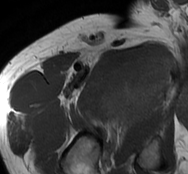
MRI of an extremity soft-tissue mass, one axial slice. Position 68 of 93 along the scan axis. MR volume resampled by the dataset authors to the PET/CT grid (not the native acquisition matrix). 3.27 mm slice thickness. 188 × 174 image matrix, field of view 184 × 170 mm. Male patient. From the clinical record (not read from this slice): histological type: undifferentiated - pleiomorphic; grade: high; site of the primary tumour: right thigh.
Outlined on this slice (expert contour drawn on MRI and transferred to this co-registered scan by the dataset authors):
- gross tumour volume including surrounding oedema: bounding box [x1, y1, x2, y2] px = [102, 46, 176, 125]
- gross tumour volume (mass): [100, 51, 174, 123]